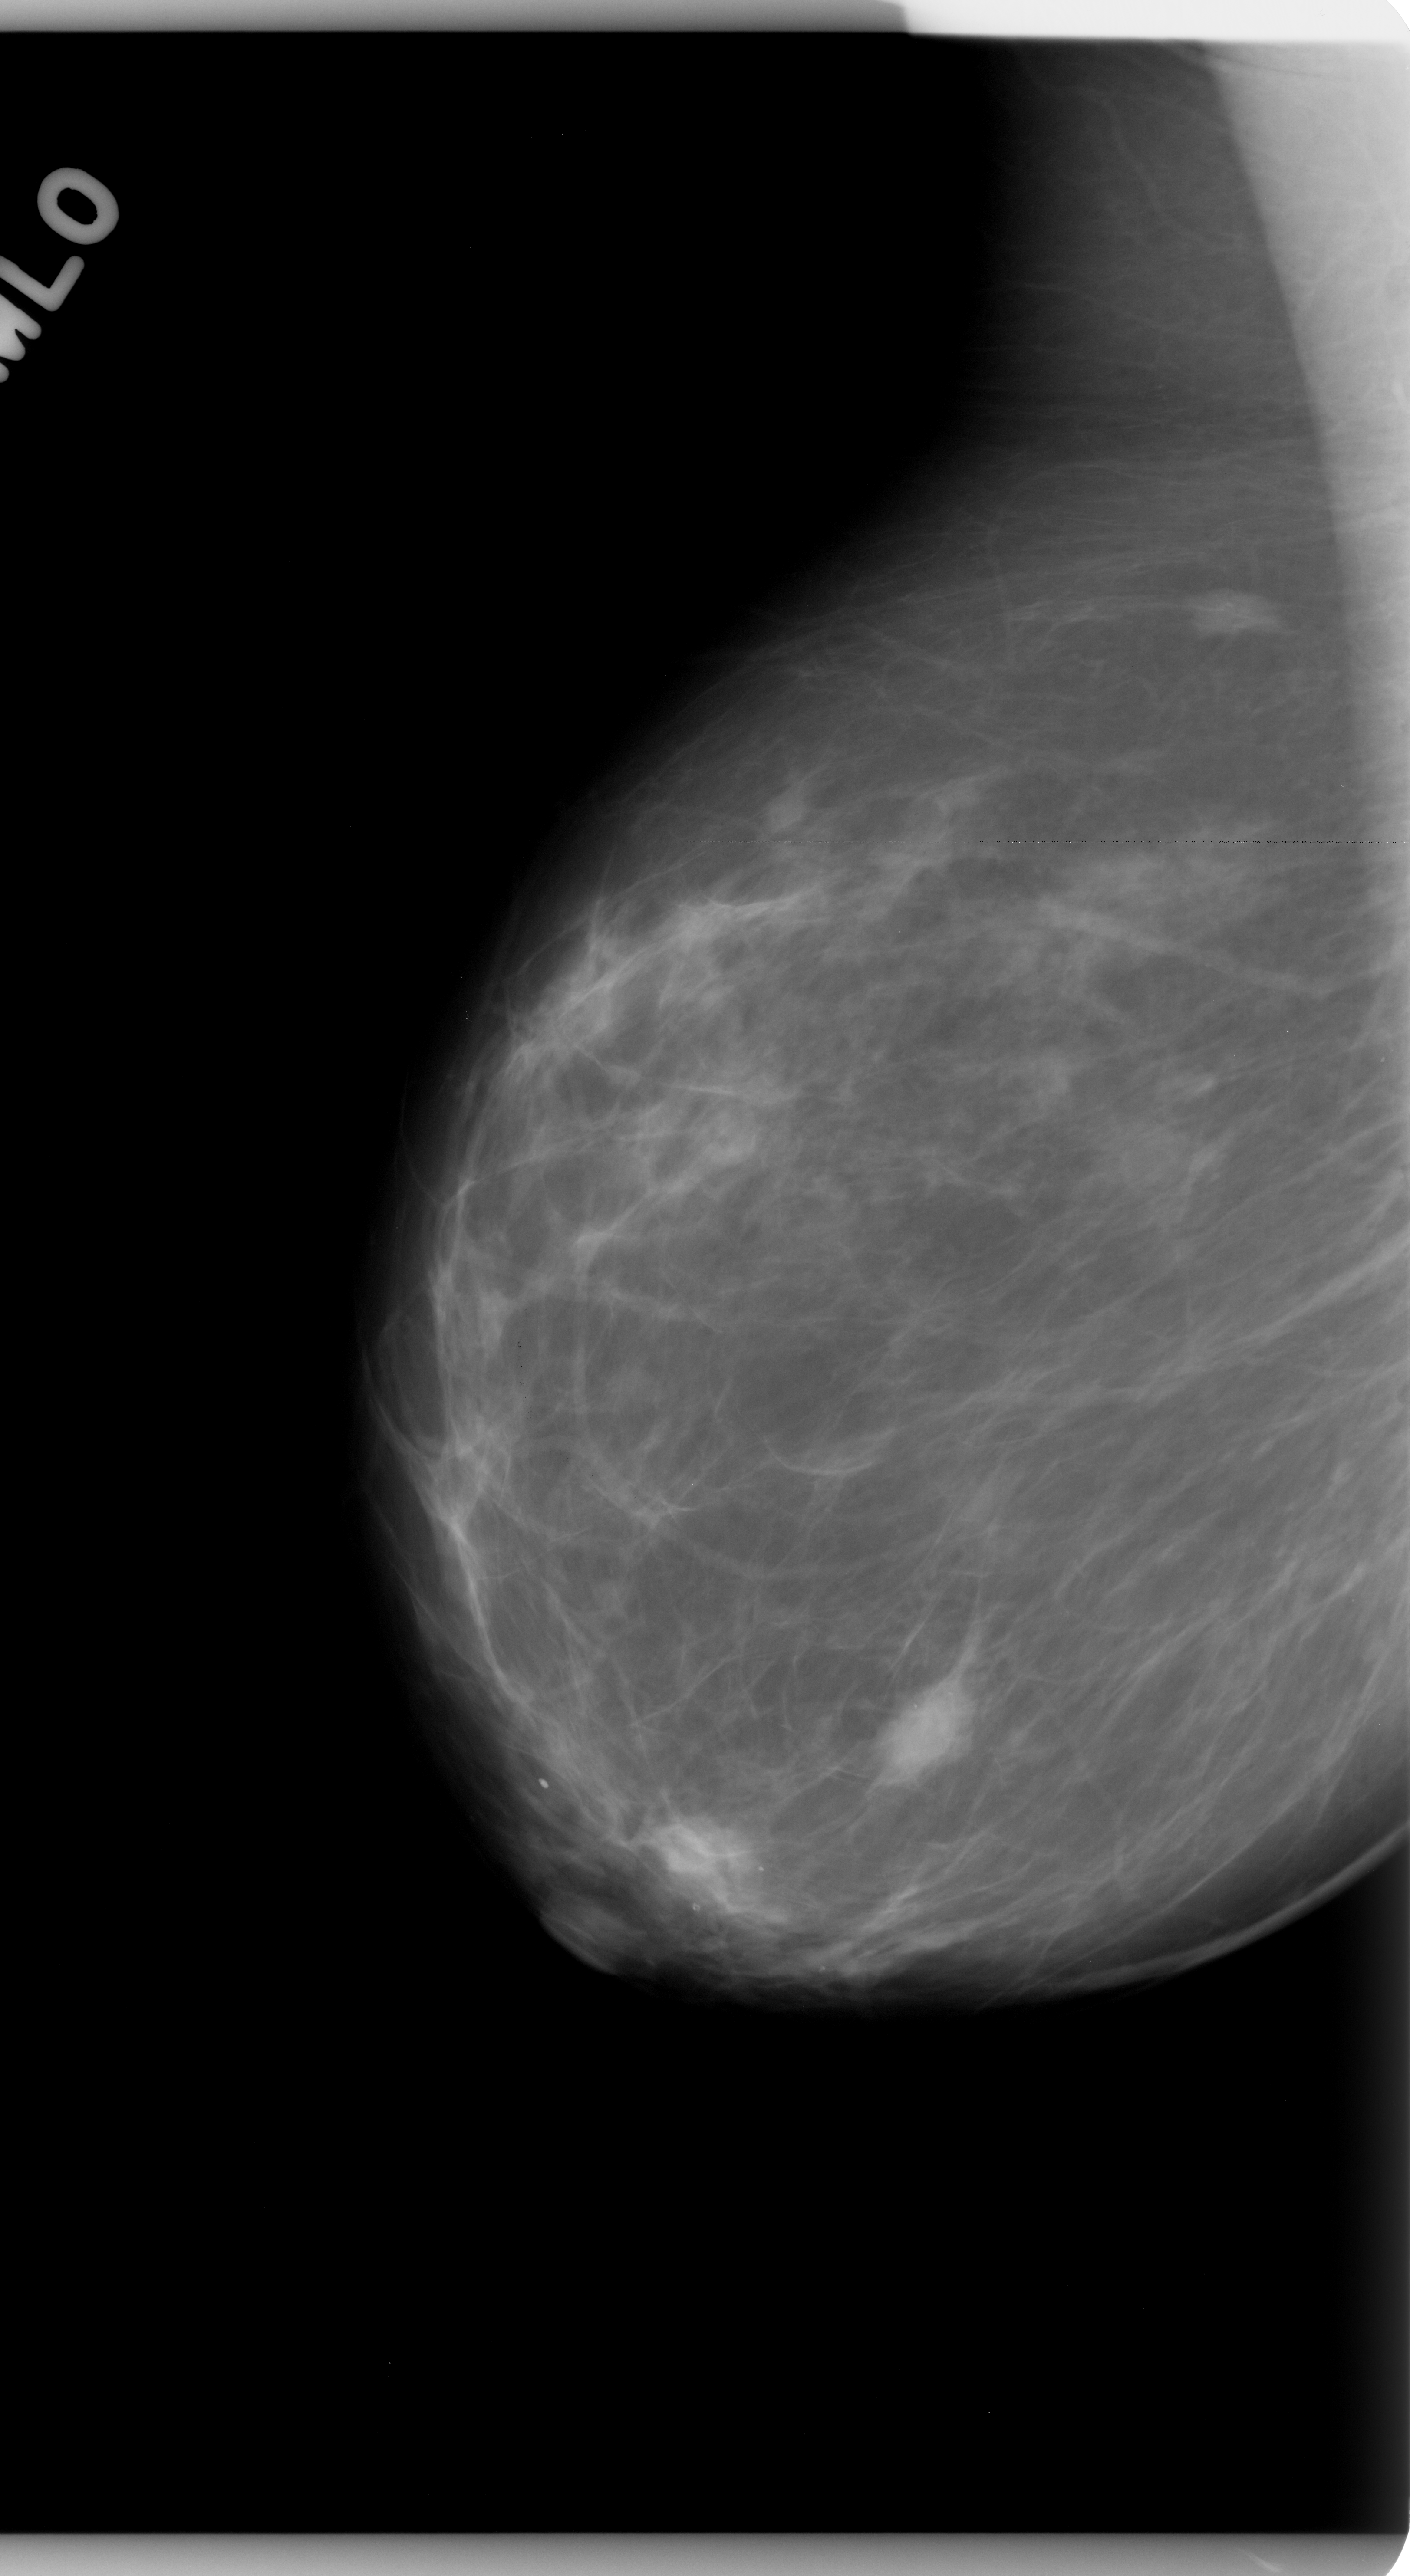
Digitized screen-film mammogram; right breast; MLO view; breast composition: almost entirely fatty (BI-RADS density category 1 of 4); 1410 × 2576 image matrix.
Expert-marked regions of interest on this film, with their recorded descriptors:
- mass, shape oval, margins microlobulated; BI-RADS assessment category 4; subtlety rating 5 on a 1 (subtle) to 5 (obvious) scale; pathology result (as recorded, not read from the image): malignant: box from (x=879, y=1613) to (x=1001, y=1772) px